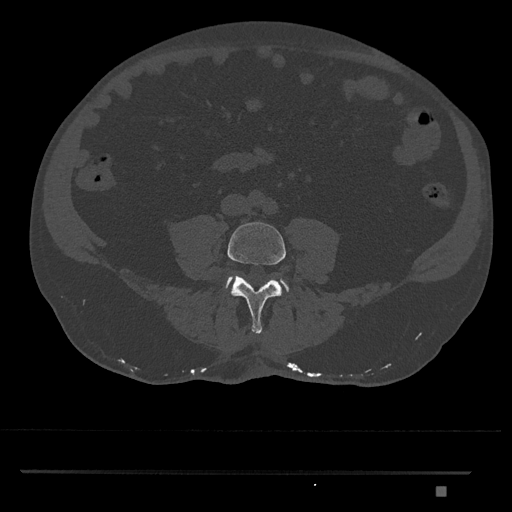
CT including the spine, one axial slice; position 605 of 1134 along the scan axis; 120 kVp; bone window (W 1800 / L 400 HU); 512 × 512 image matrix, field of view 429 × 429 mm. Male patient, age 65 years. Case-level facts recorded for this patient, not image findings: primary cancer: prostate.
Annotated regions visible in this slice (semi-automatically segmented with operator editing):
- L4 vertebra: box from (x=227, y=222) to (x=286, y=334) px
- L5 vertebra: (x=226, y=277)–(x=289, y=292)